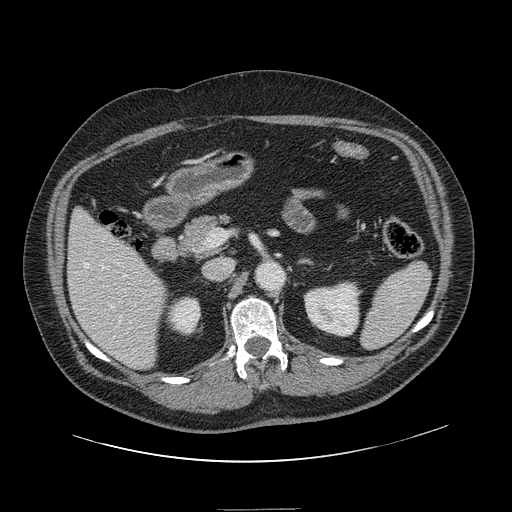
Contrast-enhanced abdominal CT, one axial slice; slice 68 of 154 in the series (ordered by position); 120 kVp; intravenous contrast given; soft-tissue window (W 400 / L 40 HU); 2.5 mm slice thickness; 512 × 512 image matrix, field of view 451 × 451 mm. Male patient, age 61 years. From the clinical record (not read from this slice): diagnosis: colorectal cancer liver metastases, imaged before liver resection.
Annotated regions visible in this slice (manually delineated by an expert):
- hepatic veins: box from (x=84, y=263) to (x=123, y=324) px
- liver: (x=69, y=211)–(x=166, y=369)
- planned liver remnant (the part of the liver to remain after resection): (x=69, y=210)–(x=166, y=365)
- portal vein (with intrahepatic branches): (x=129, y=321)–(x=131, y=324)